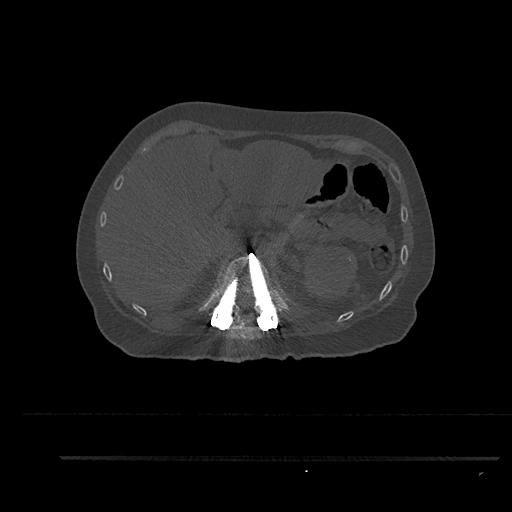
CT including the spine, one axial slice; reconstruction kernel Br40s/3; bone window (W 1800 / L 400 HU); 0.5 mm slice thickness; 512 × 512 image matrix, field of view 408 × 408 mm. Female patient, age 44 years. From the clinical record (not read from this slice): primary cancer: renal.
Structures marked on this image (semi-automatically segmented with operator editing):
- T11 vertebra: bounding box <232,322,244,329> (left, top, right, bottom; pixels)
- T12 vertebra: <213,254,282,319>